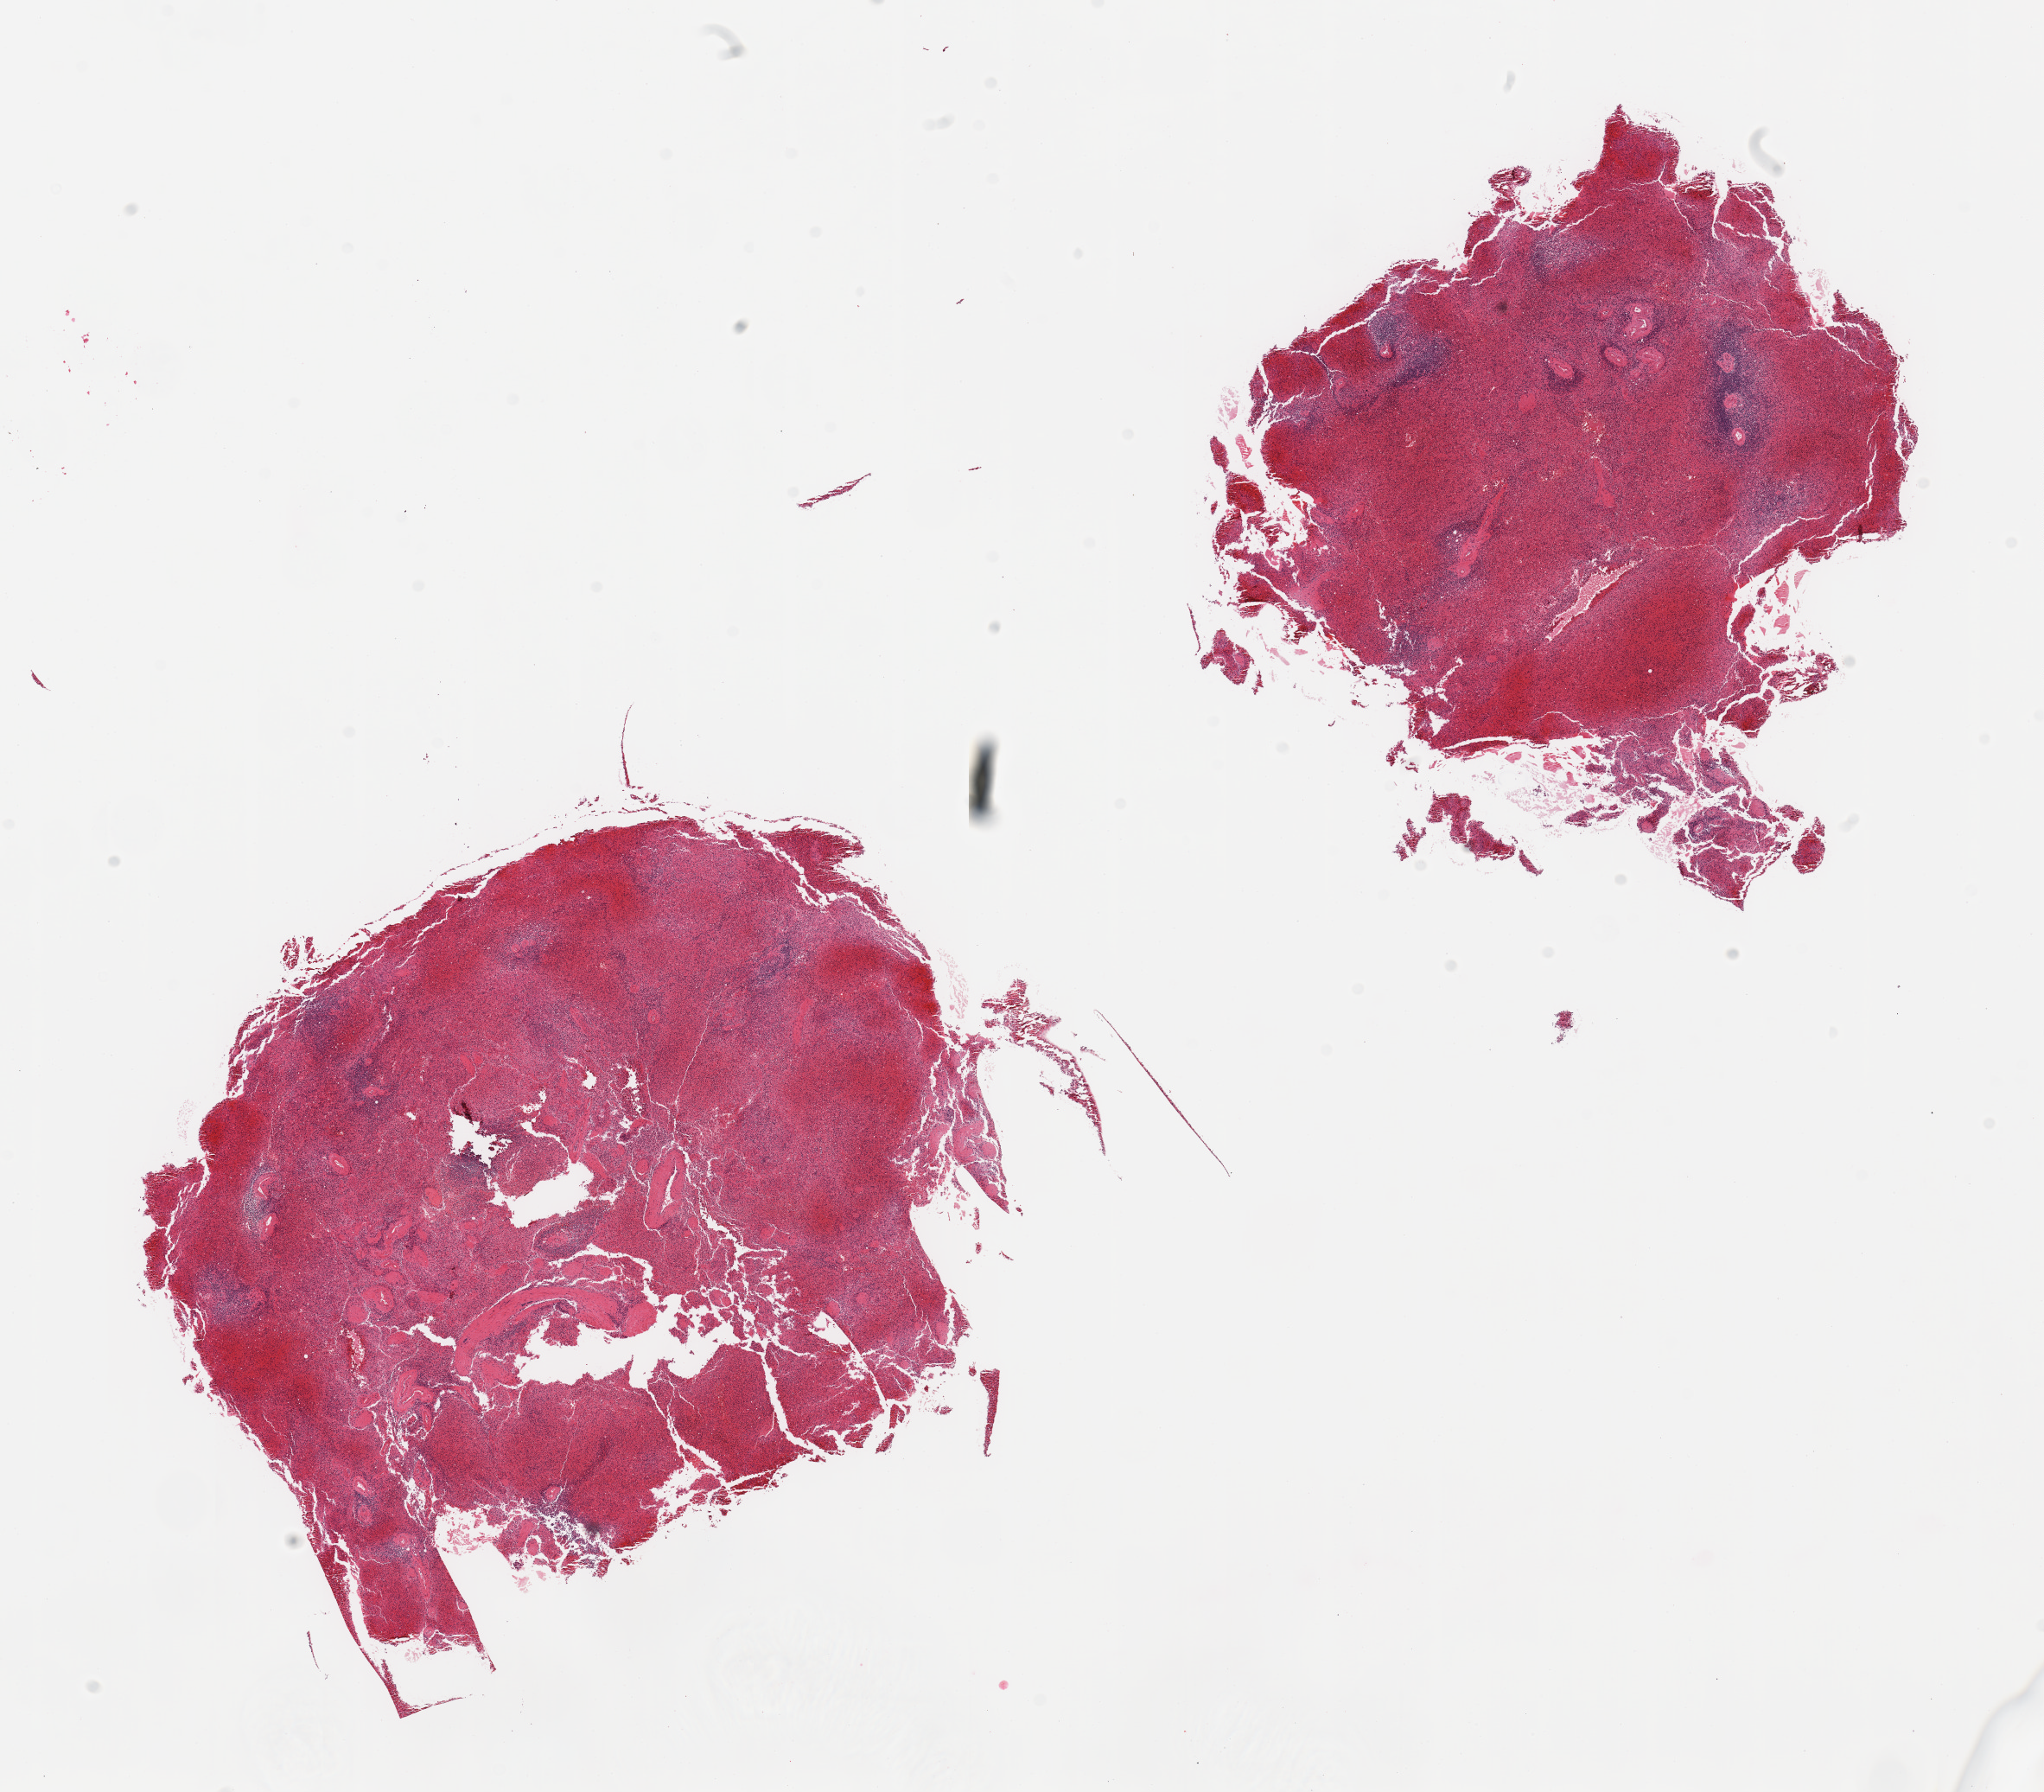
Whole-slide image, H&E stain, brightfield — a low-resolution overview of the entire scanned area, about 18.7 x 16.4 mm; PAXgene-fixed, paraffin-embedded tissue; section of spleen (target tissue); tissue donor sample. Donor sex: male.
Pathologist's review note for this sample: 2 pieces, marked congestion.